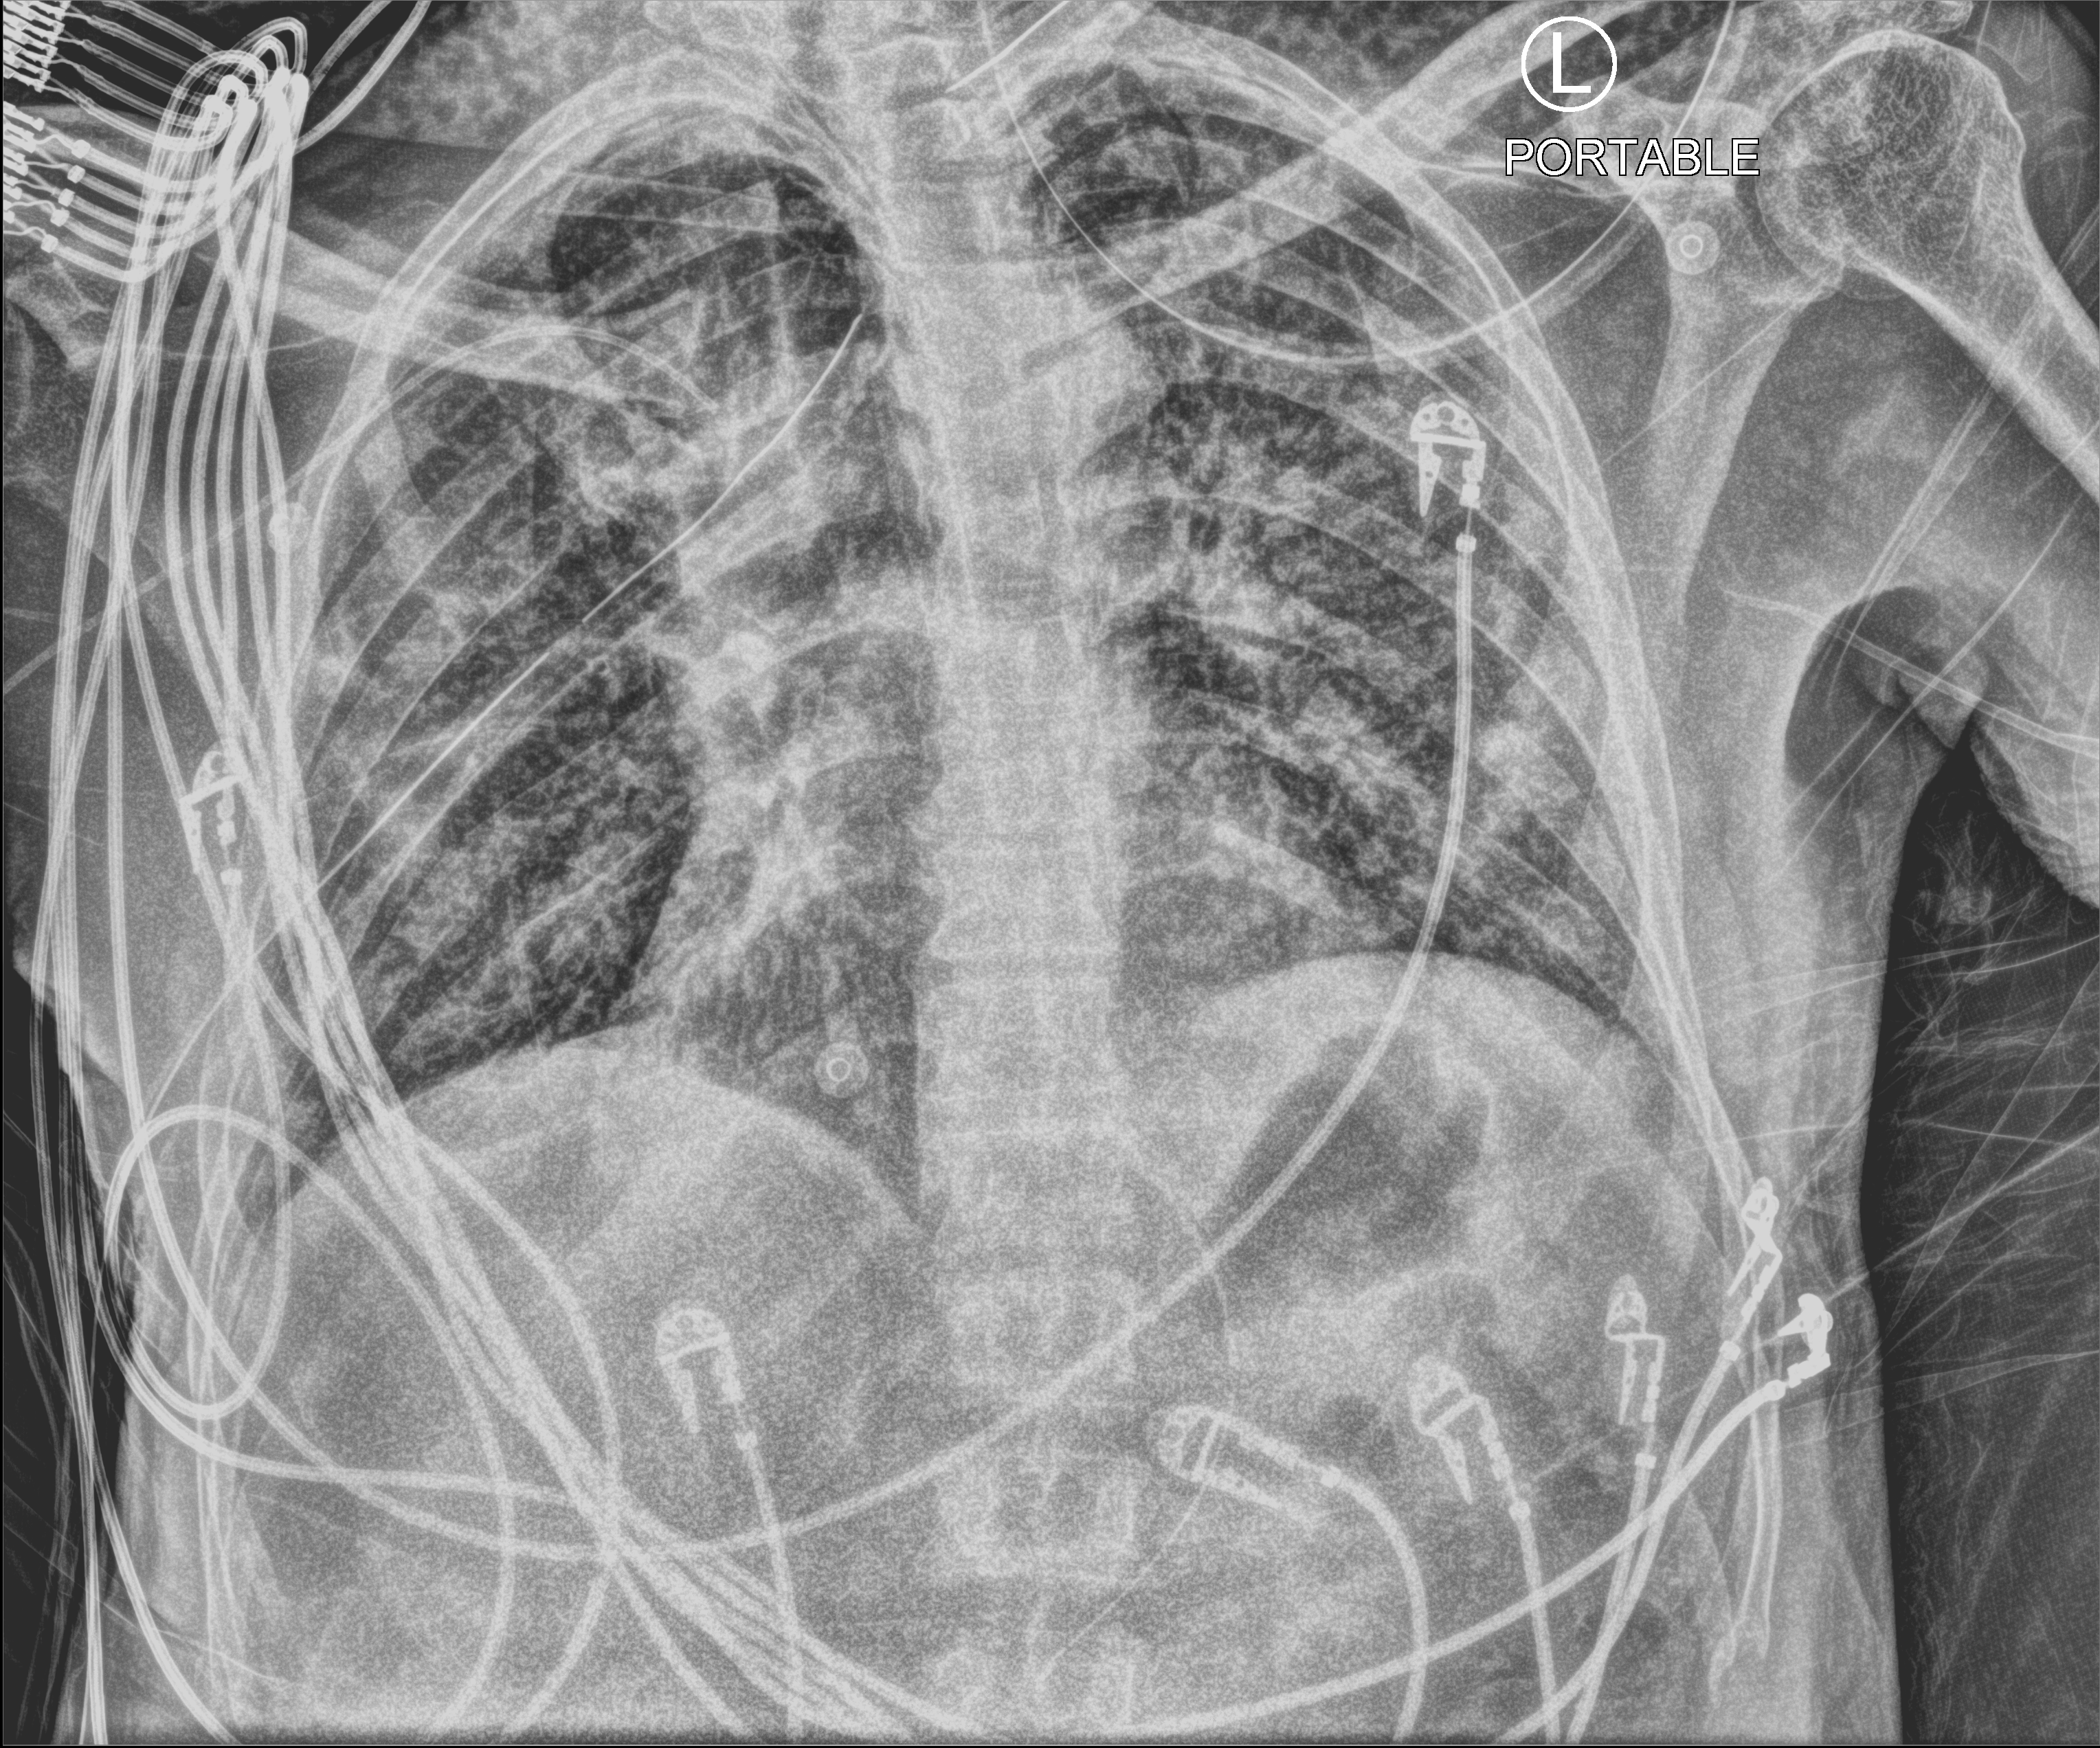
Bedside chest radiograph (computed radiography); anteroposterior (AP) projection. Male patient hospitalised with COVID-19, age 18–59 years.
Hospital-stay facts (about this admission, not read from this image; timing relative to this image not recorded):
- admitted to intensive care during this hospital stay: yes